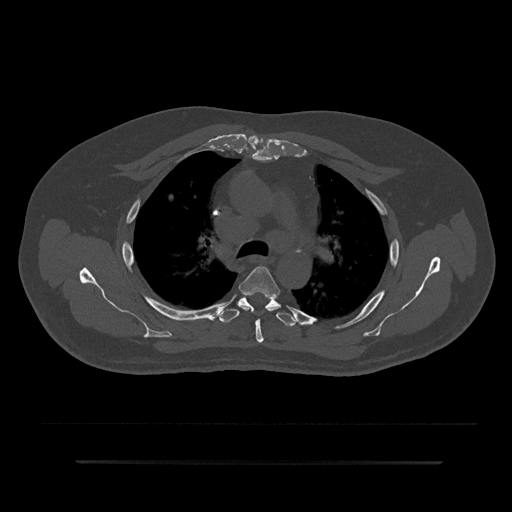
CT including the spine, one axial slice. Reconstruction kernel Br40s/3. 120 kVp. Bone window (W 1800 / L 400 HU). 0.5 mm slice thickness. 512 × 512 image matrix, field of view 464 × 464 mm. Patient: male, 59 years. Case-level facts recorded for this patient, not image findings: primary cancer: bile ducts.
Outlined on this slice (semi-automatic segmentation, software-assisted and operator-edited):
- T4 vertebra: bounding box <239,266,280,343> (left, top, right, bottom; pixels)
- T5 vertebra: <219,296,297,327>